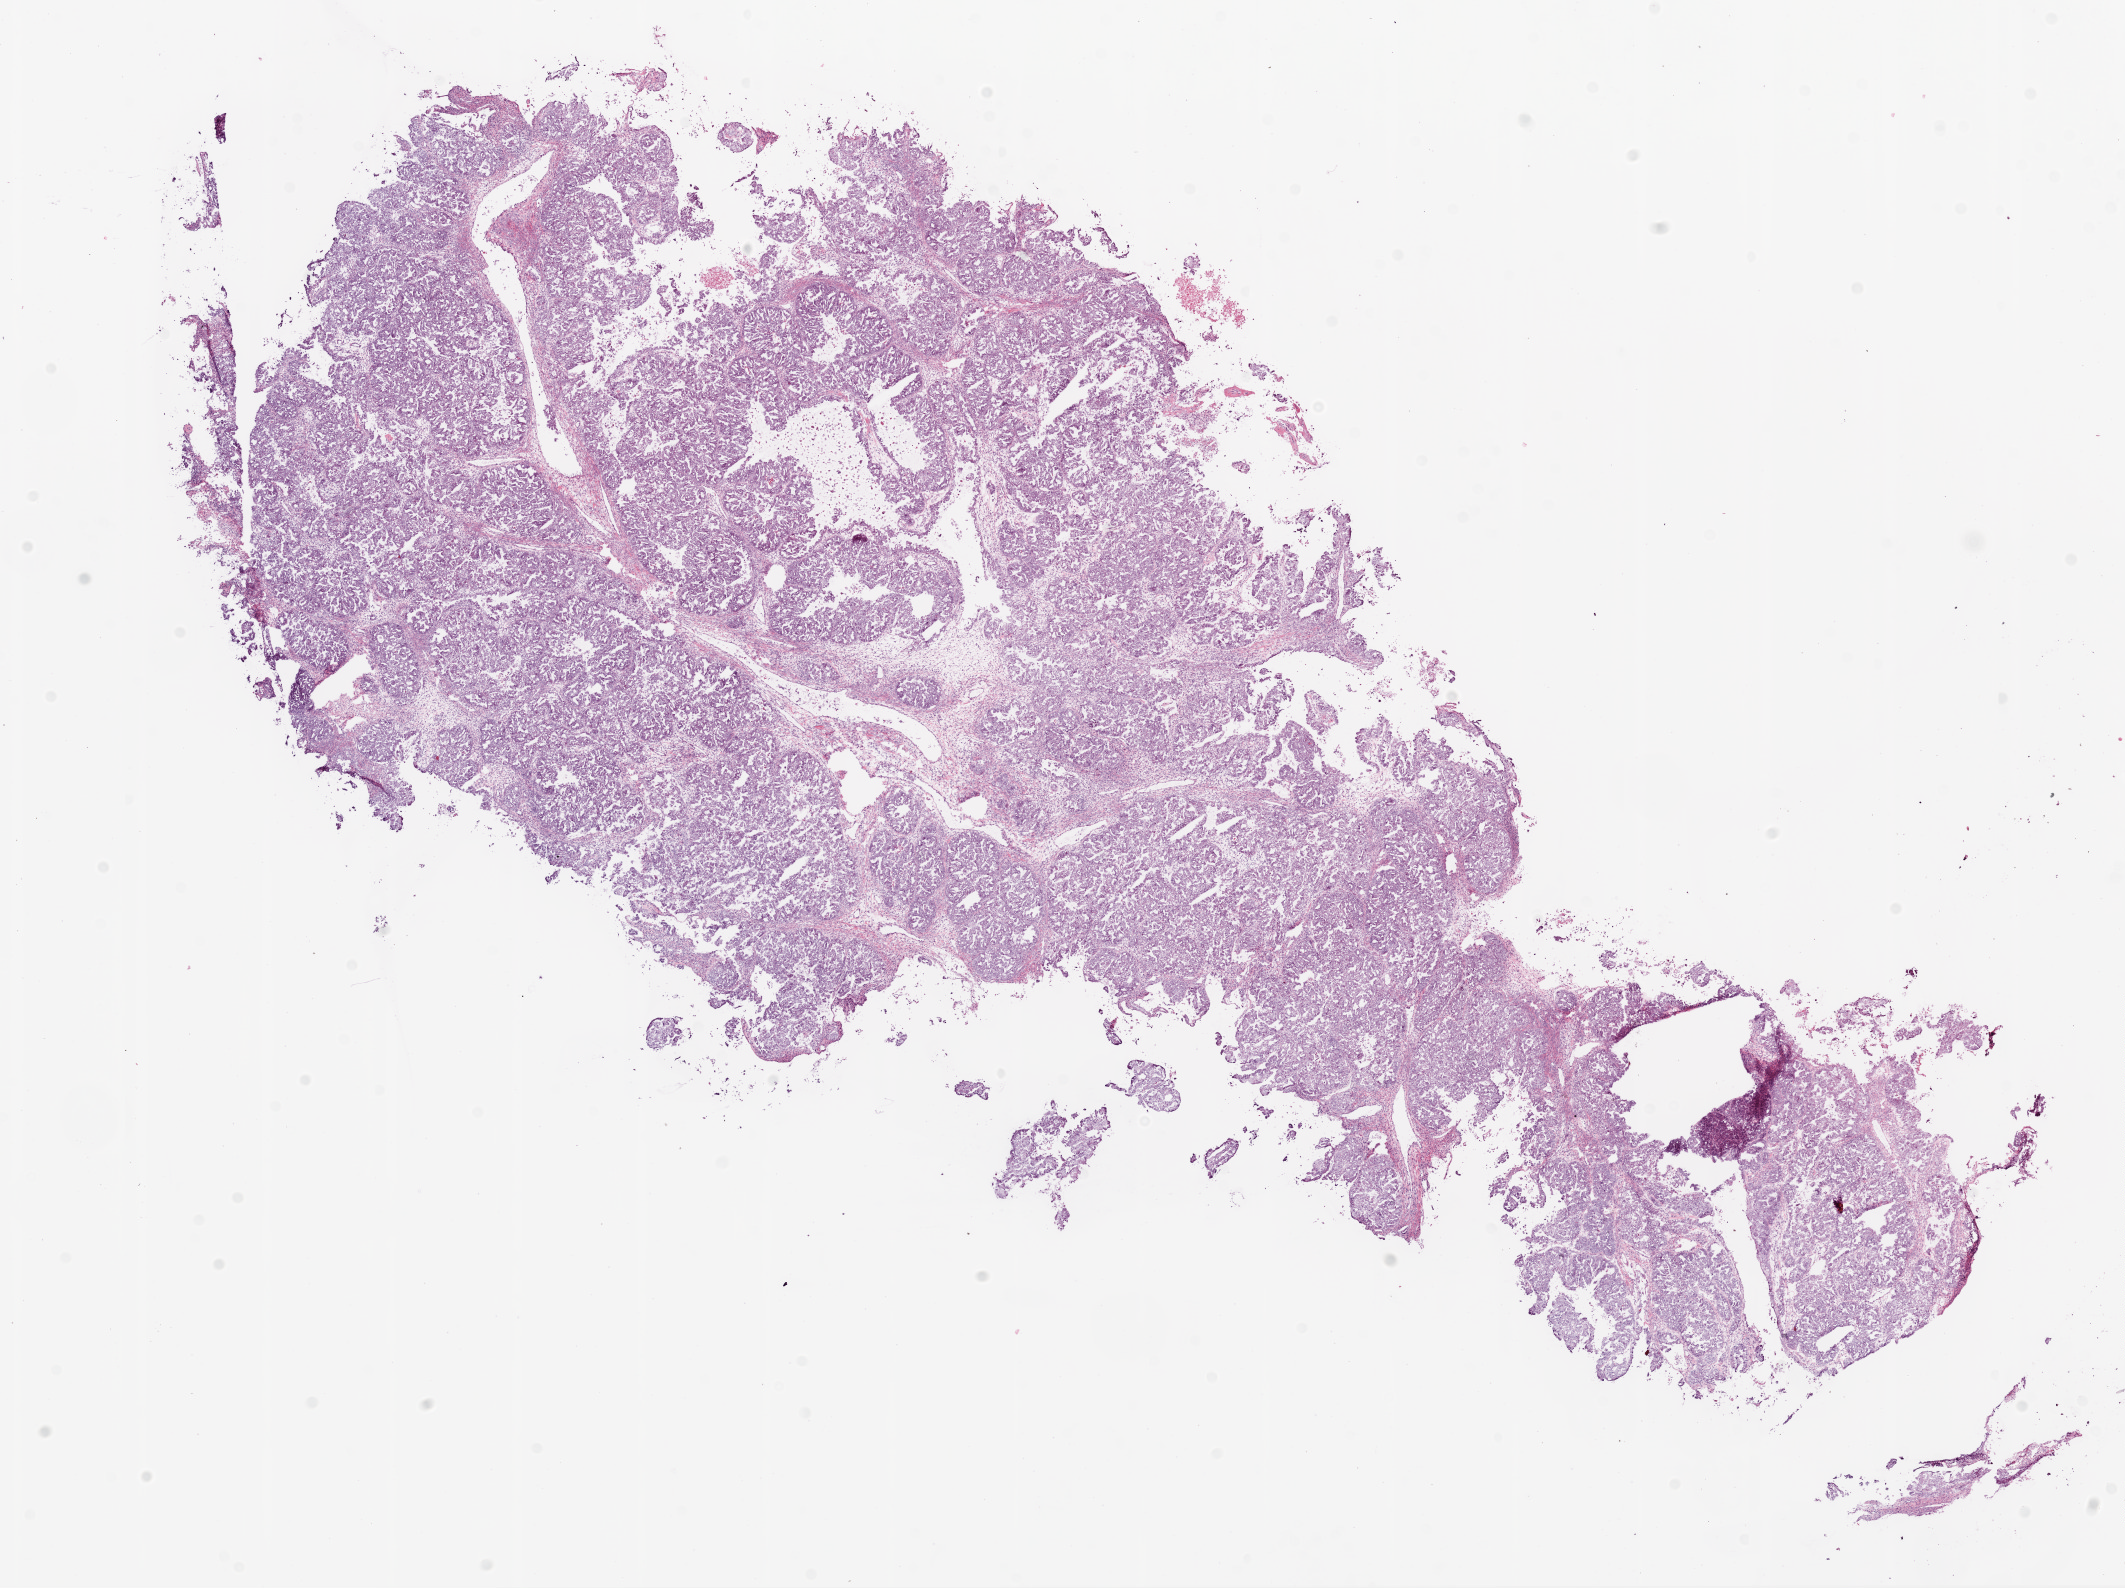
H&E-stained whole-slide image, a low-resolution overview of the entire scanned area, about 17.1 x 12.7 mm (slide scanned at 20x). Frozen section from the top of the tissue portion. Sample: primary tumour, ovary. Female, age 48 years at initial diagnosis.
Diagnosis: Serous cystadenocarcinoma, NOS.